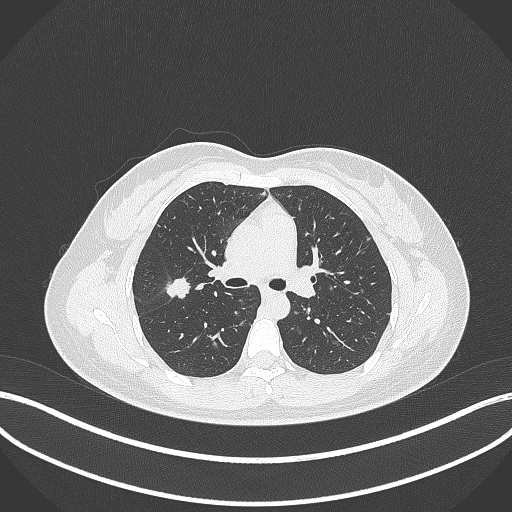
Chest CT, one axial slice. Slice 207 of 307 in the series (ordered by position). Lung window (W 1500 / L -600 HU). 512 × 512 image matrix, field of view 400 × 400 mm. Patient: female, 33 years. From the clinical record (not read from this slice): clinical TNM (as recorded): T1c N0 M0; histopathological grade: G2-G3.
Outlined on this slice (bounding box drawn by a radiologist):
- lung tumour (recorded histology: adenocarcinoma): box from (x=165, y=274) to (x=194, y=302) px